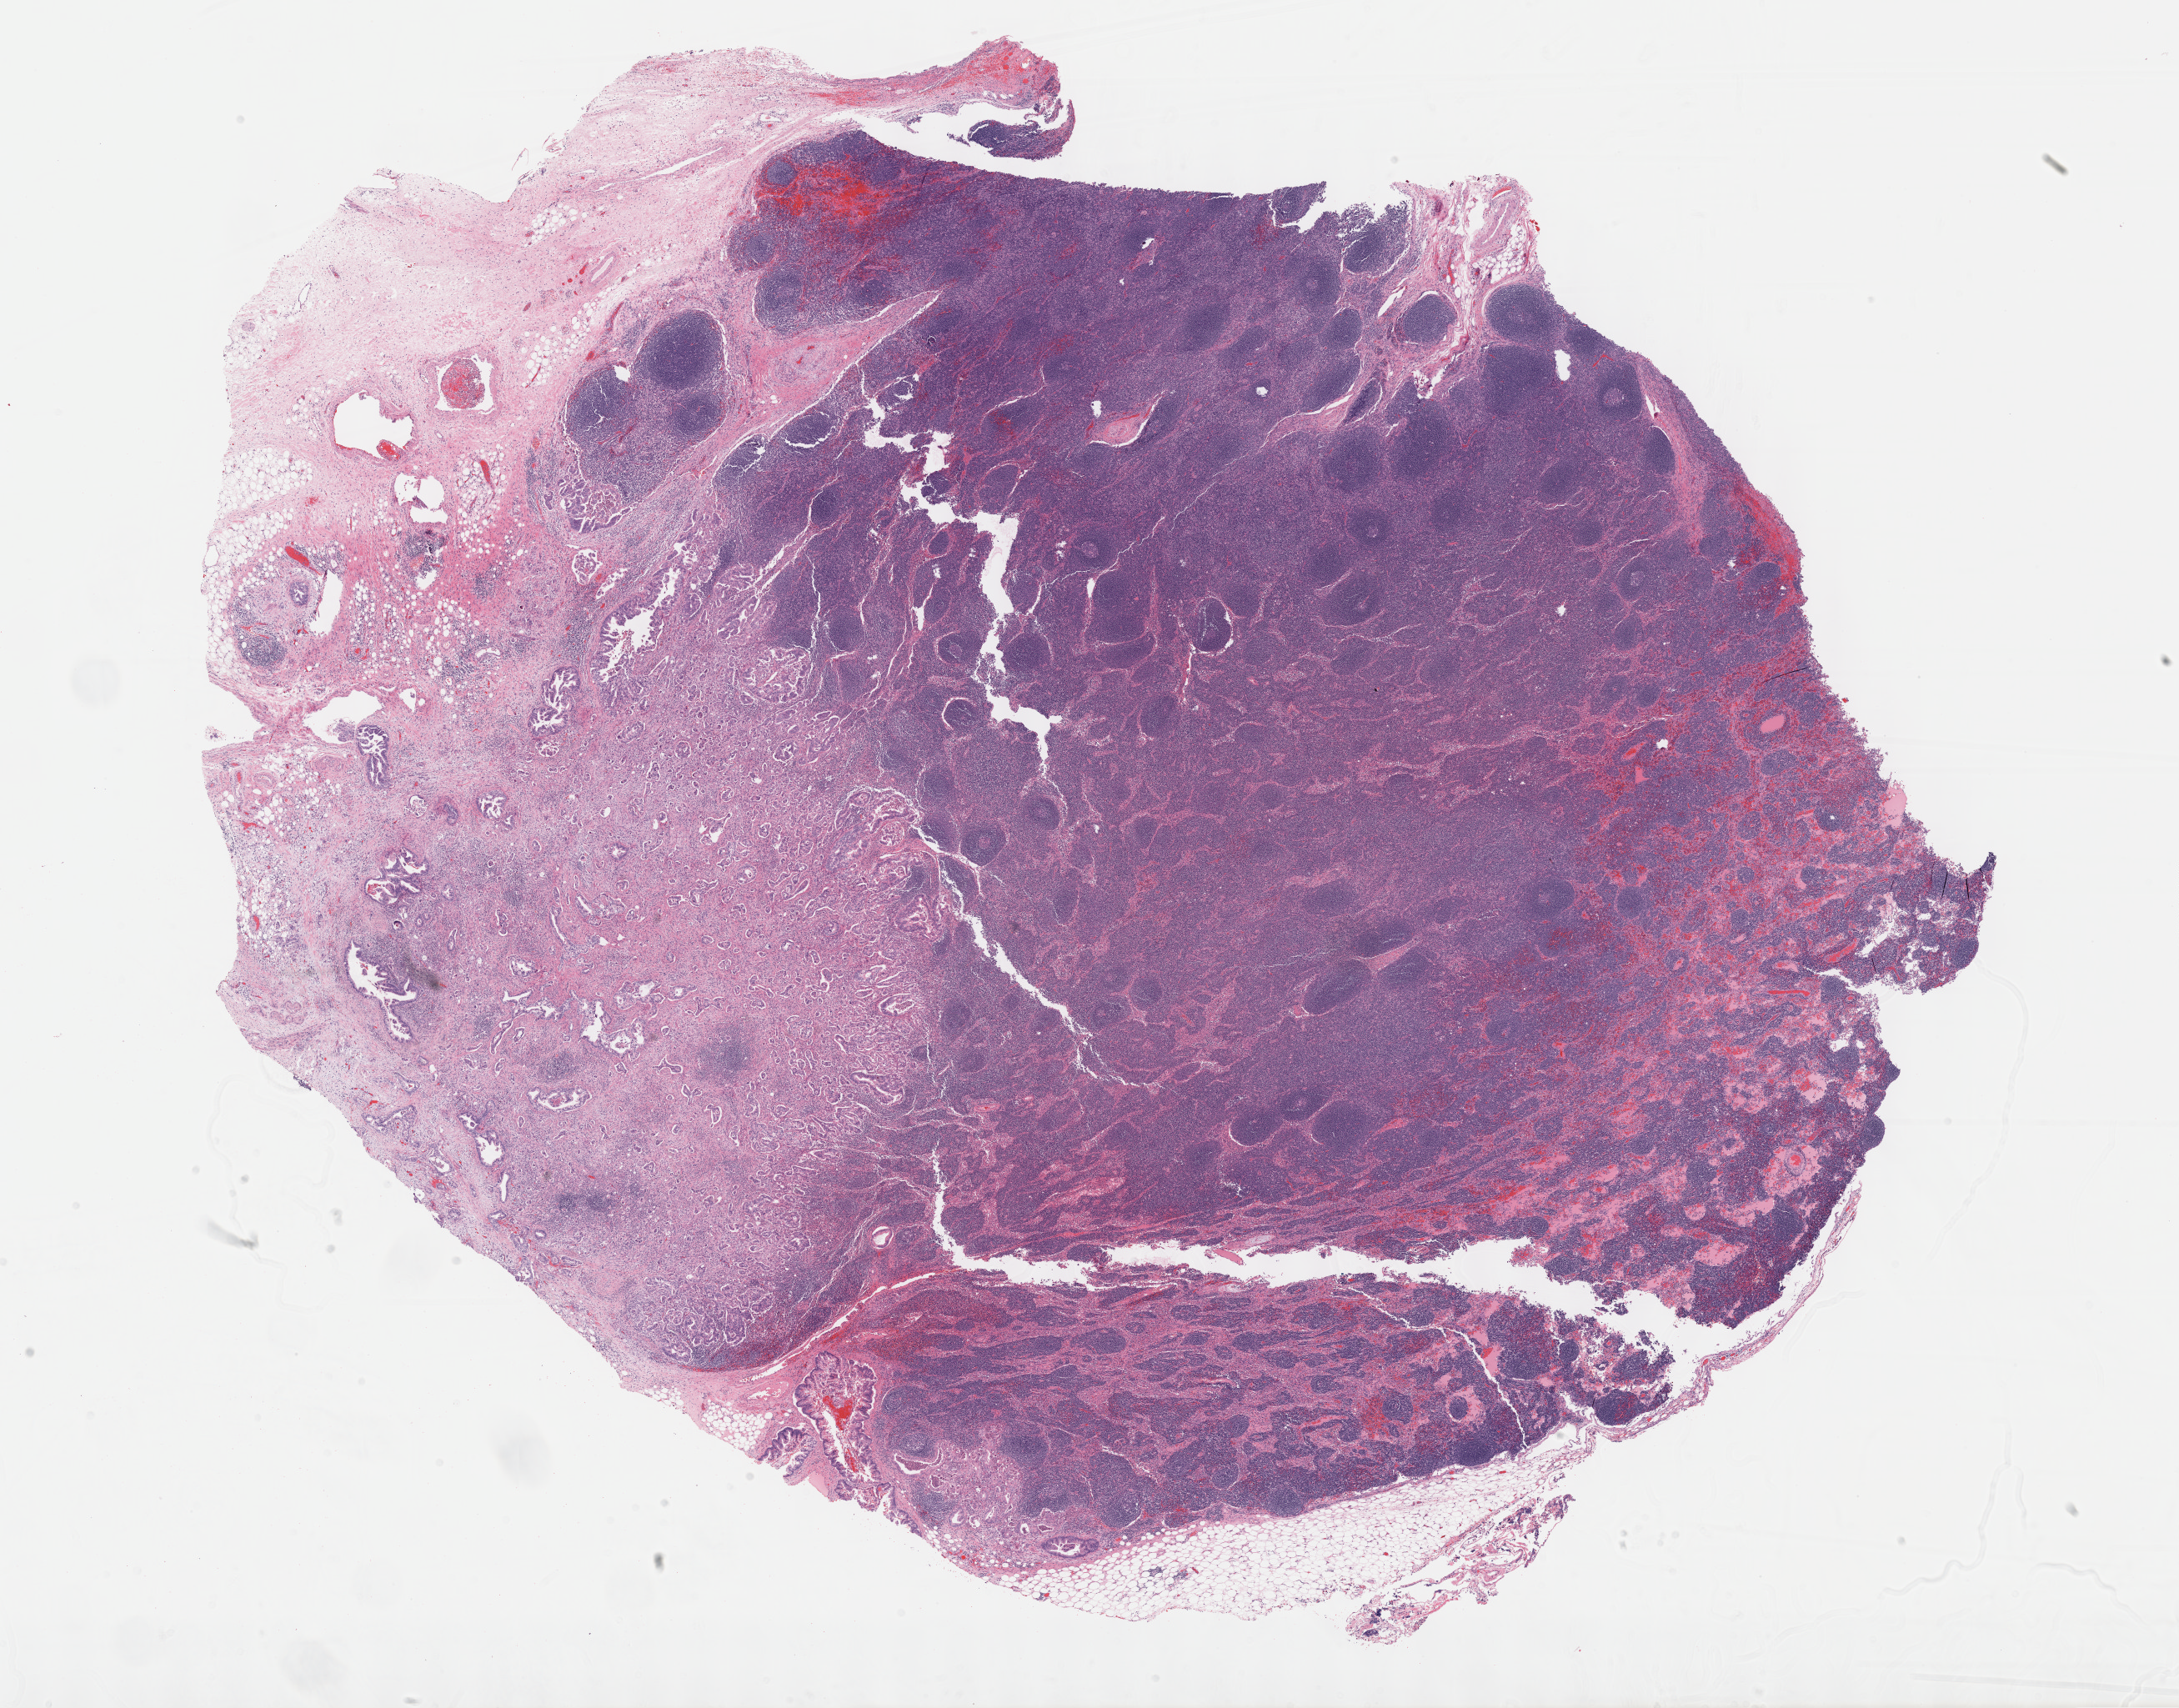
Whole-slide histology image, Hematoxylin and eosin (H&E) stained, low-resolution overview of the scanned area, about 21.1 x 16.6 mm. FFPE section. Primary tumour sample from the pancreas. Patient: female, age at initial diagnosis 50 years. Histologic grade: G2 (moderately differentiated).
* AJCC pathologic stage: IIB (7th edition)
* lymph nodes positive (case pathology): 10 of 33 examined
* histologic diagnosis: Infiltrating duct carcinoma, NOS (head of pancreas)